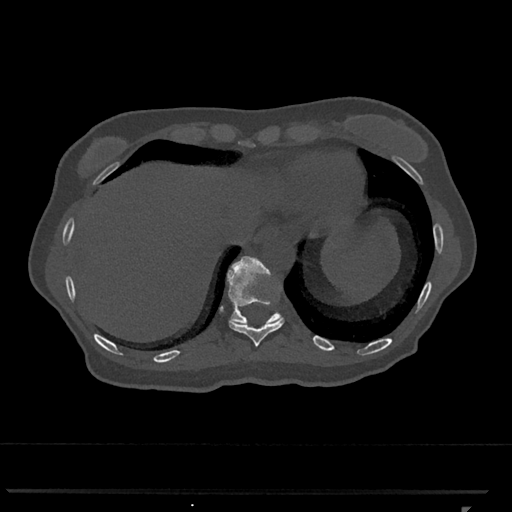
CT including the spine, one axial slice. Position 553 of 793 along the scan axis. Reconstruction kernel Br40s/3. Bone window (W 1800 / L 400 HU). 0.5 mm slice thickness. 512 × 512 image matrix. Female patient, age 62 years. From the clinical record (not read from this slice): primary cancer: renal.
Annotated regions visible in this slice (semi-automatic segmentation, software-assisted and operator-edited):
- T10 vertebra: bounding box [x1, y1, x2, y2] px = [229, 318, 285, 347]
- T11 vertebra: [227, 256, 283, 325]